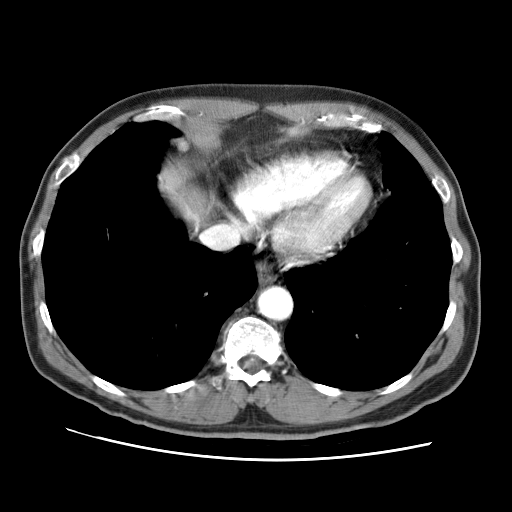
Contrast-enhanced abdominal CT (liver protocol), one axial slice. Reconstruction kernel STANDARD. Soft-tissue window (W 400 / L 40 HU). 2.5 mm slice thickness. 512 × 512 image matrix, field of view 360 × 360 mm. From the clinical record (not read from this slice): diagnosis: hepatocellular carcinoma (patient treated with transarterial chemoembolisation; whether this scan precedes or follows treatment is not stated here); TNM stage (as recorded): Stage-II.
Outlined on this slice (semi-automatically segmented with operator editing):
- liver parenchyma outside the tumour (the mass and vessels are separate outlines, so this box may not span the whole liver): bounding box (x1, y1, x2, y2) in pixels: (182, 196, 202, 221)
- liver vessels: (194, 216, 196, 218)